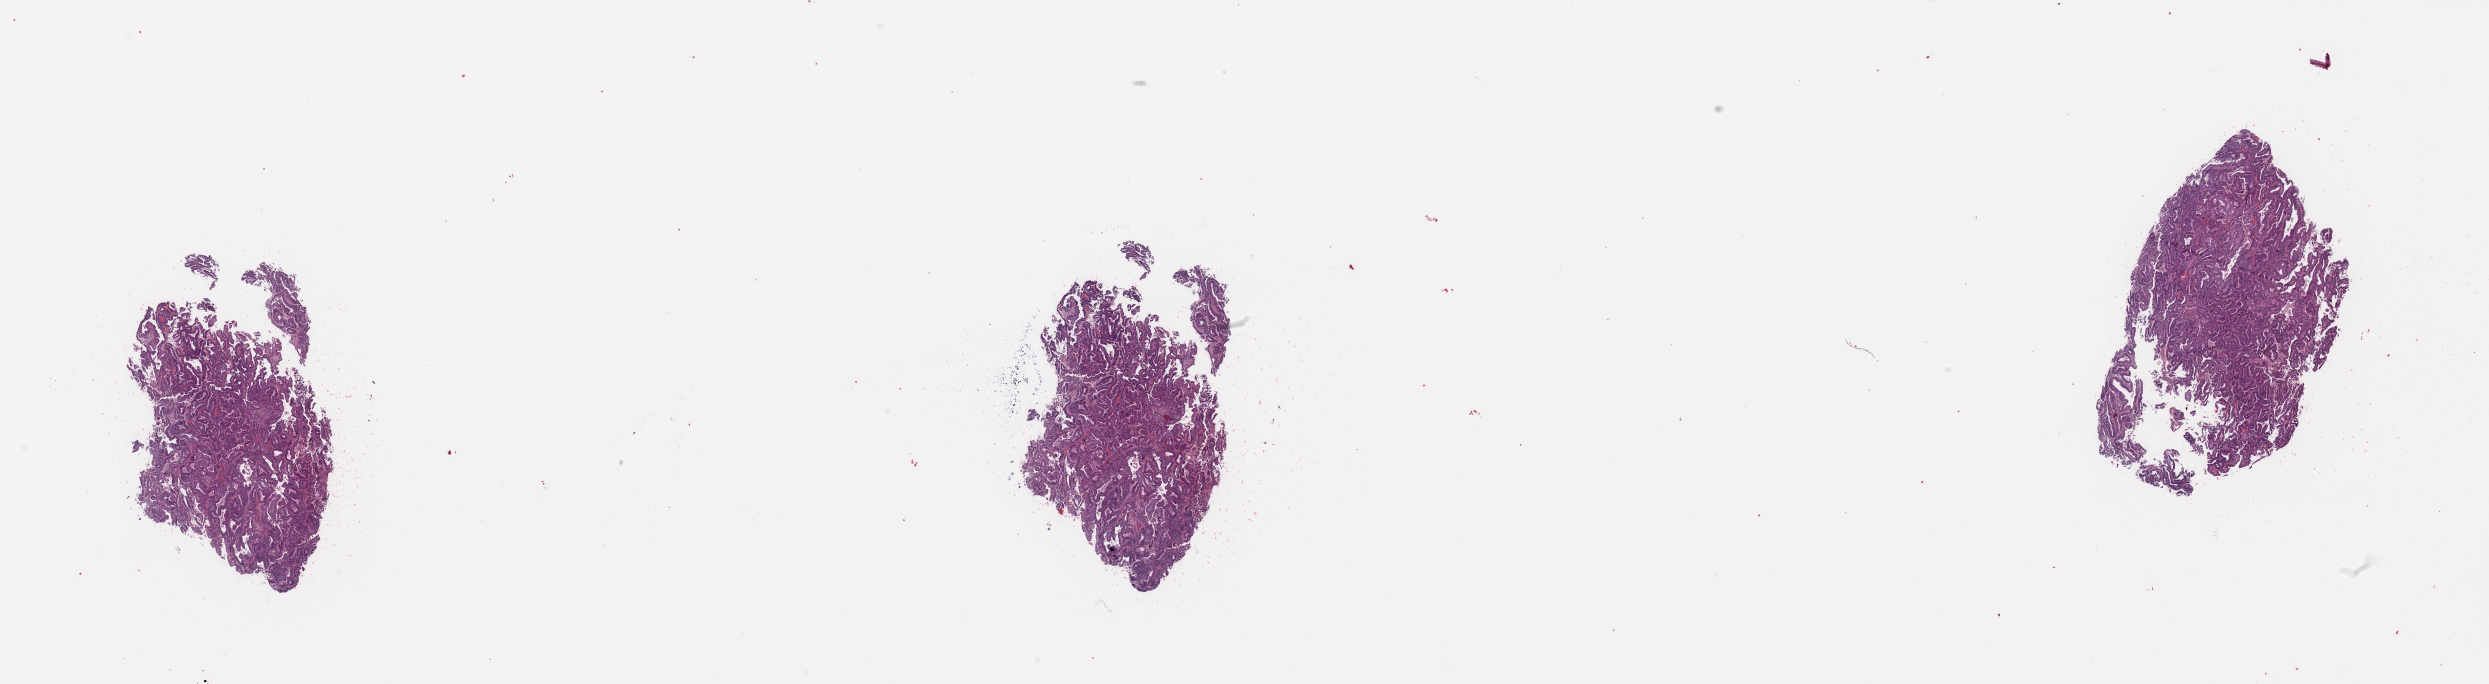
Hematoxylin and eosin (H&E) stained whole-slide image, shown as a low-resolution overview of the whole scanned area (about 39.4 x 10.8 mm, from a 20x scan). Uterus, tumour tissue. Female, 53 y/o.
Histologic diagnosis: Endometrioid adenocarcinoma, NOS.